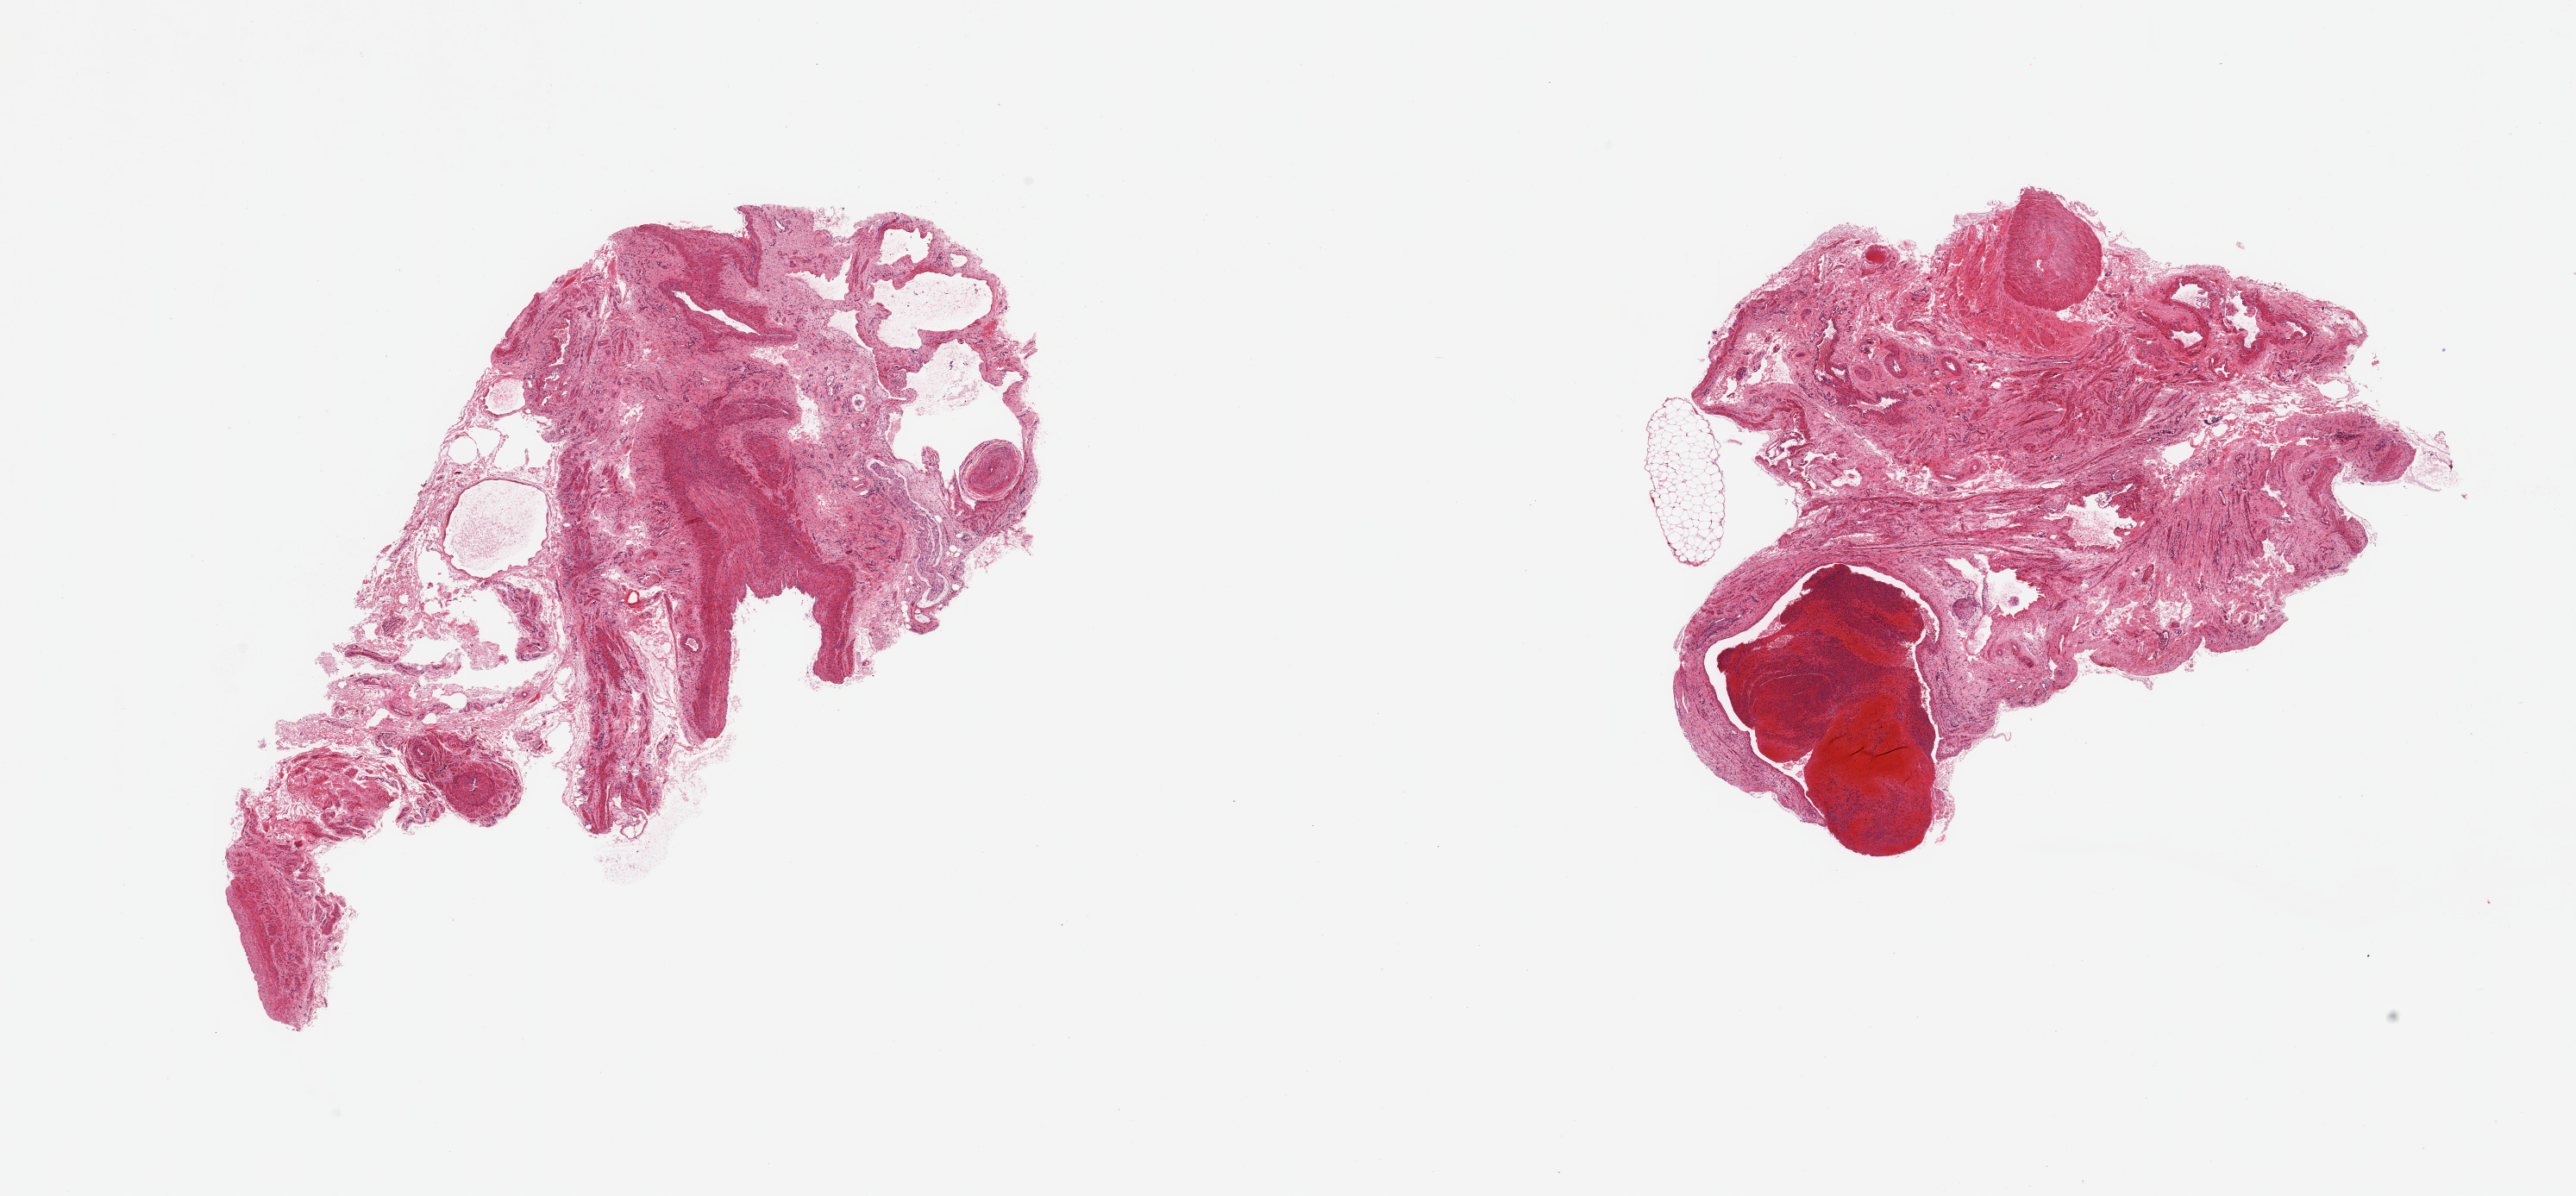
Whole-slide image, haematoxylin and eosin stain — low-resolution overview of the scanned area, about 23.6 x 11.0 mm (slide scanned at 20x).
* specimen: PAXgene-fixed paraffin-embedded (PFPE) section; section of ovary (target tissue); tissue donor sample